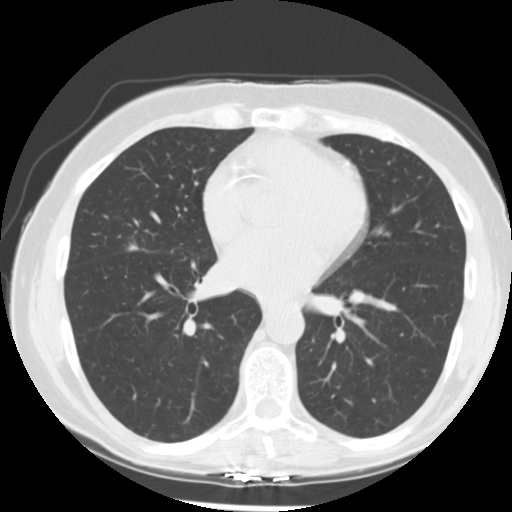
Chest CT (low-dose screening protocol), one axial image, first (baseline) screen, lung window (W 1500 / L -600 HU), 2.5 mm slice thickness, 120 kVp, slice 130 of 255 in the series, 512 × 512 image matrix, field of view 320 × 320 mm. Female, age 66 years at enrolment. Former smoker at enrolment.
Expert-annotated lung lesion, box from (x=114, y=227) to (x=169, y=267) px. Reader record for this screening exam (exam-level; its link to the box is not recorded): non-calcified nodule or mass ≥4 mm, right middle lobe, 15 × 13 mm, poorly defined margins, soft tissue attenuation. Official screen result: positive, change unspecified: nodule(s) >= 4 mm or enlarging nodule(s), mass(es), or other non-specific abnormalities suspicious for lung cancer. Later outcome: lung cancer diagnosed 27 days after this screen — adenocarcinoma, NOS, right middle lobe, undifferentiated (G4), stage IIIA (AJCC 6th edition), 18 mm at pathology.